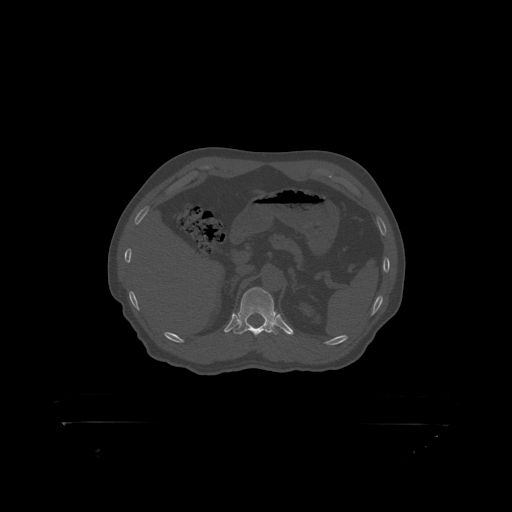
CT including the spine, one axial slice; position 354 of 399 along the scan axis; reconstruction kernel STANDARD; 120 kVp; bone window (W 1800 / L 400 HU); 1.25 mm slice thickness; 512 × 512 image matrix, field of view 650 × 650 mm. Male patient, age 46 years. From the clinical record (not read from this slice): primary cancer: skin.
Annotated regions visible in this slice (semi-automatically segmented with operator editing):
- T12 vertebra: box from (x=234, y=287) to (x=279, y=319) px